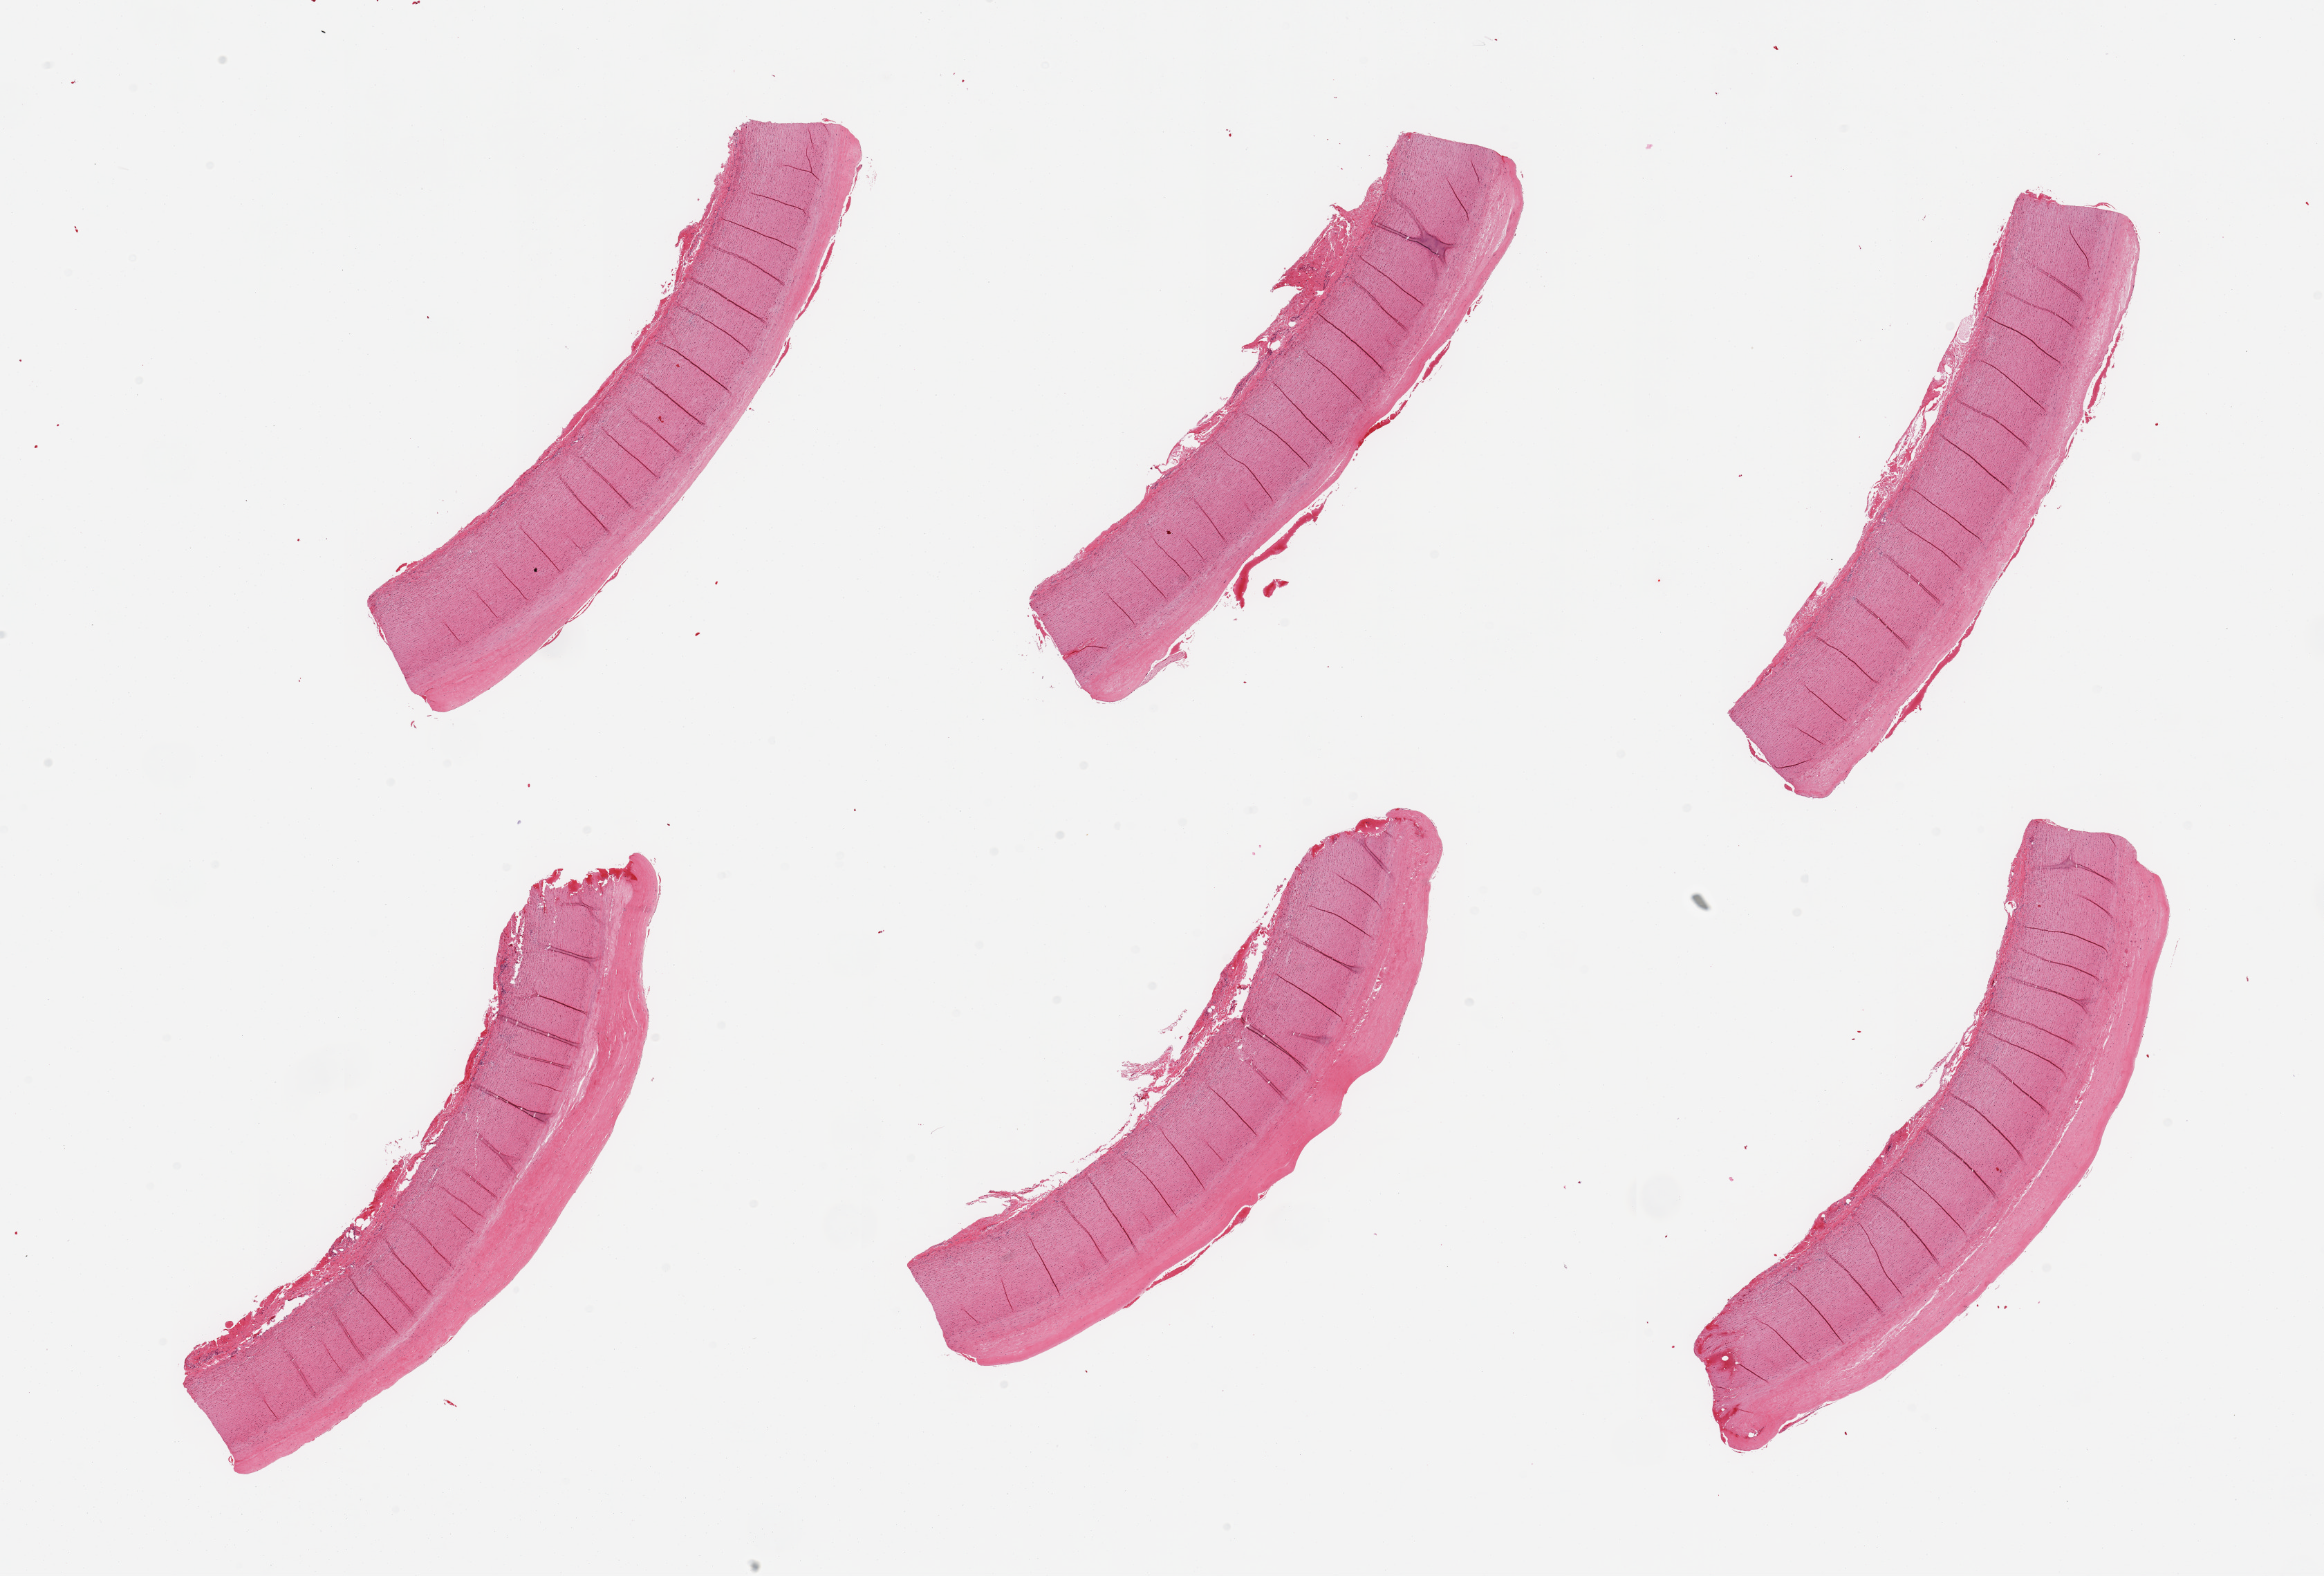
Whole-slide image, haematoxylin and eosin stain, brightfield, low-resolution overview of the scanned area, about 26.6 x 18.0 mm, PAXgene-fixed, paraffin-embedded tissue, sampled site (target tissue): aorta, donor tissue sample. Donor sex: male.
Reviewer comment on this tissue sample: 6 pieces, atherosis up to ~0.6mm.